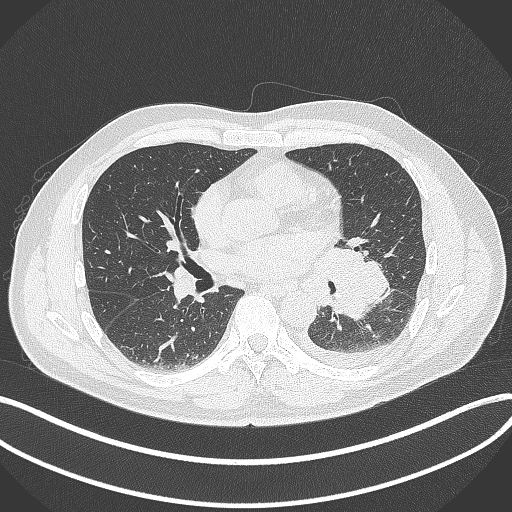
Chest CT, one axial slice; slice 180 of 342 in the series (ordered by position); lung window (W 1500 / L -600 HU); 512 × 512 image matrix, field of view 400 × 400 mm. Male patient, age 58 years. Case-level facts recorded for this patient, not image findings: clinical TNM (as recorded): T3 N1 M1b; histopathological grade: G3.
Outlined on this slice (bounding box drawn by a radiologist):
- lung tumour (recorded histology: small cell carcinoma): box from (x=310, y=238) to (x=391, y=322) px